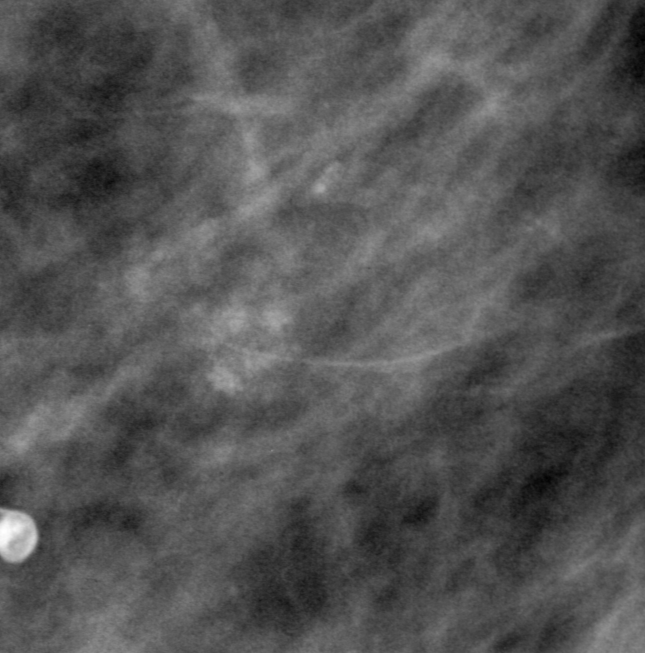
Crop from a digitized film mammogram around one marked abnormality, right breast, MLO view, BI-RADS breast density category 2 (scale 1–4).
Marked abnormality: calcifications, morphology amorphous, distribution clustered; BI-RADS assessment category 3; pathology (as recorded): malignant.